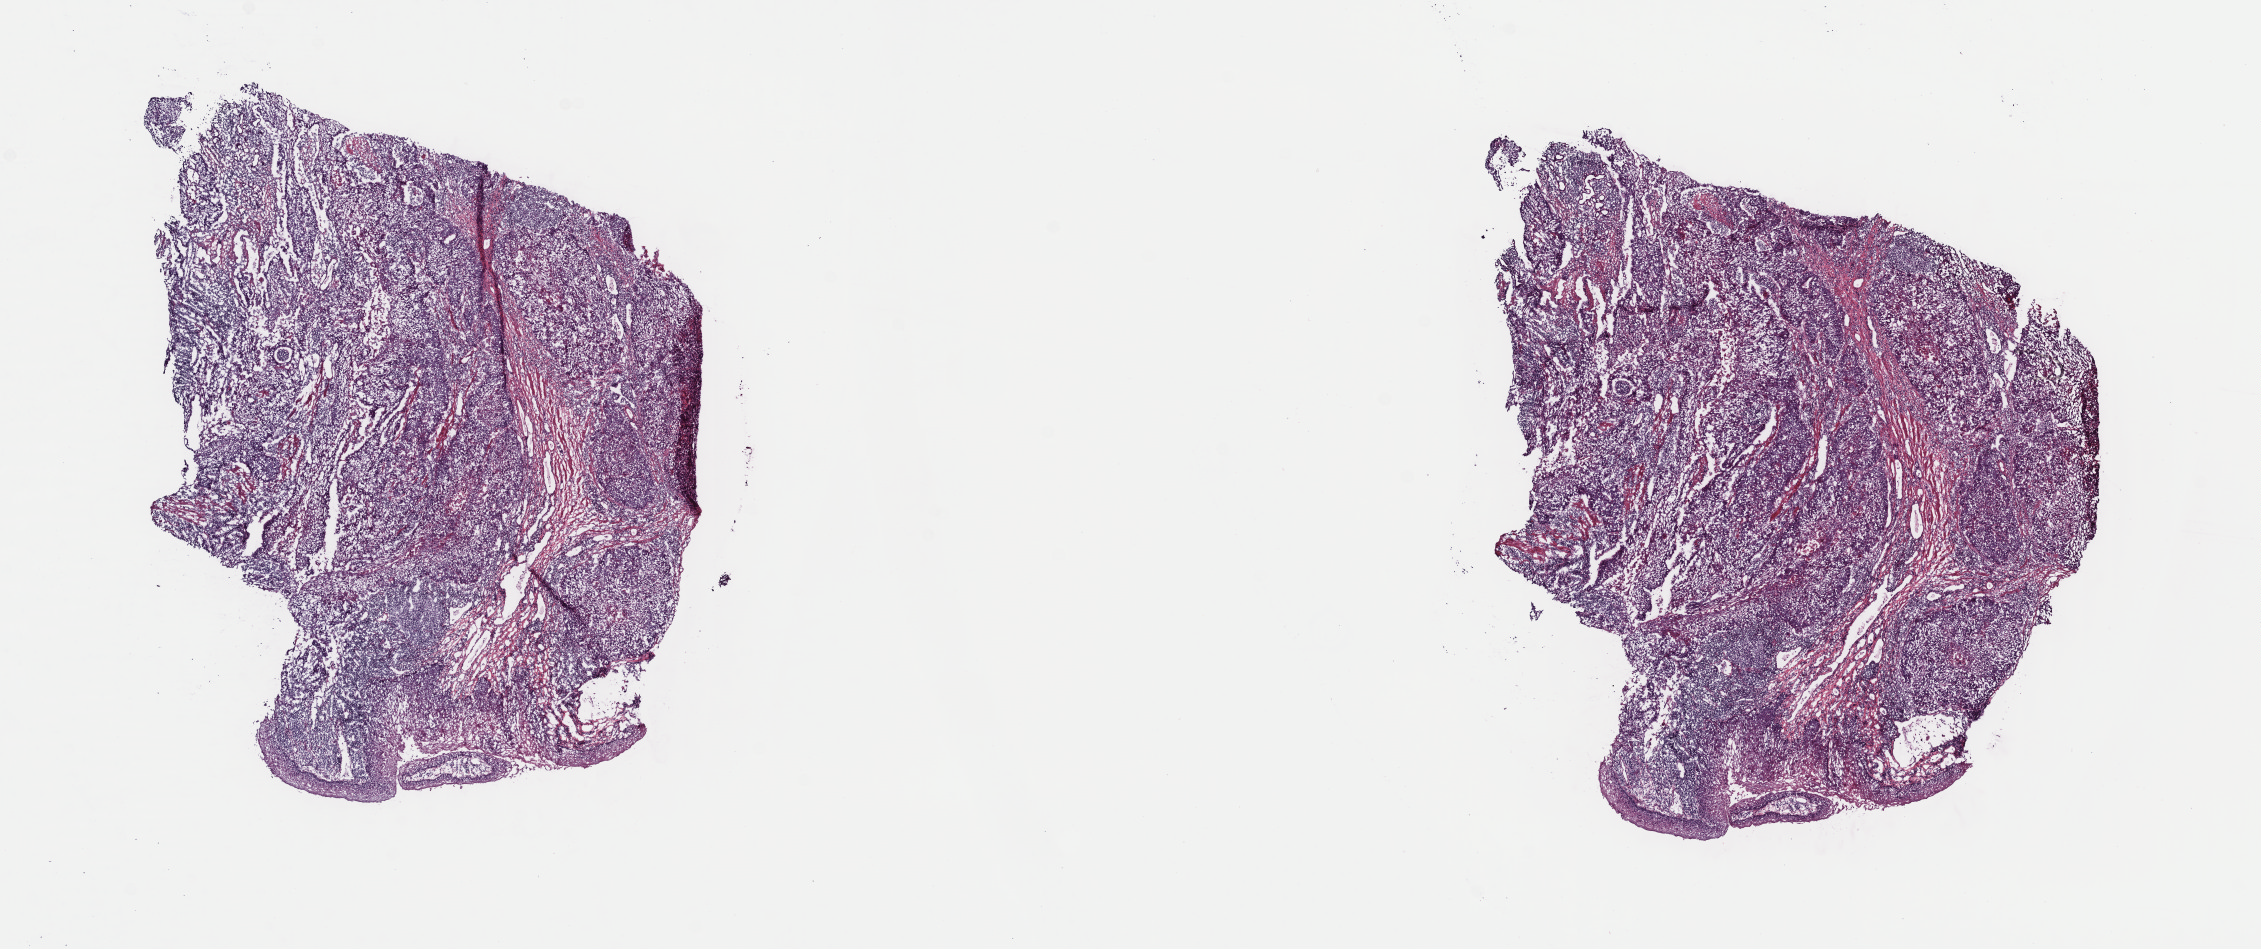
Whole-slide histology image, H&E, a low-resolution overview of the entire scanned area, about 17.8 x 7.5 mm (from a 40x scan); frozen section from the top of the tissue portion; primary tumour sample from the esophagus. Patient: male, age at initial diagnosis 48 years. Histologic grade: G2 (moderately differentiated). Composition of this section per pathologist review: tumour cells 95%, tumour nuclei 75%, normal cells 5%, stromal cells 0%, necrosis 0%. Inflammatory infiltration, as recorded: lymphocyte infiltration 4%, monocyte infiltration 0%, neutrophil infiltration 1%.
• AJCC pathologic stage: IIB
• histologic diagnosis: Squamous cell carcinoma, NOS